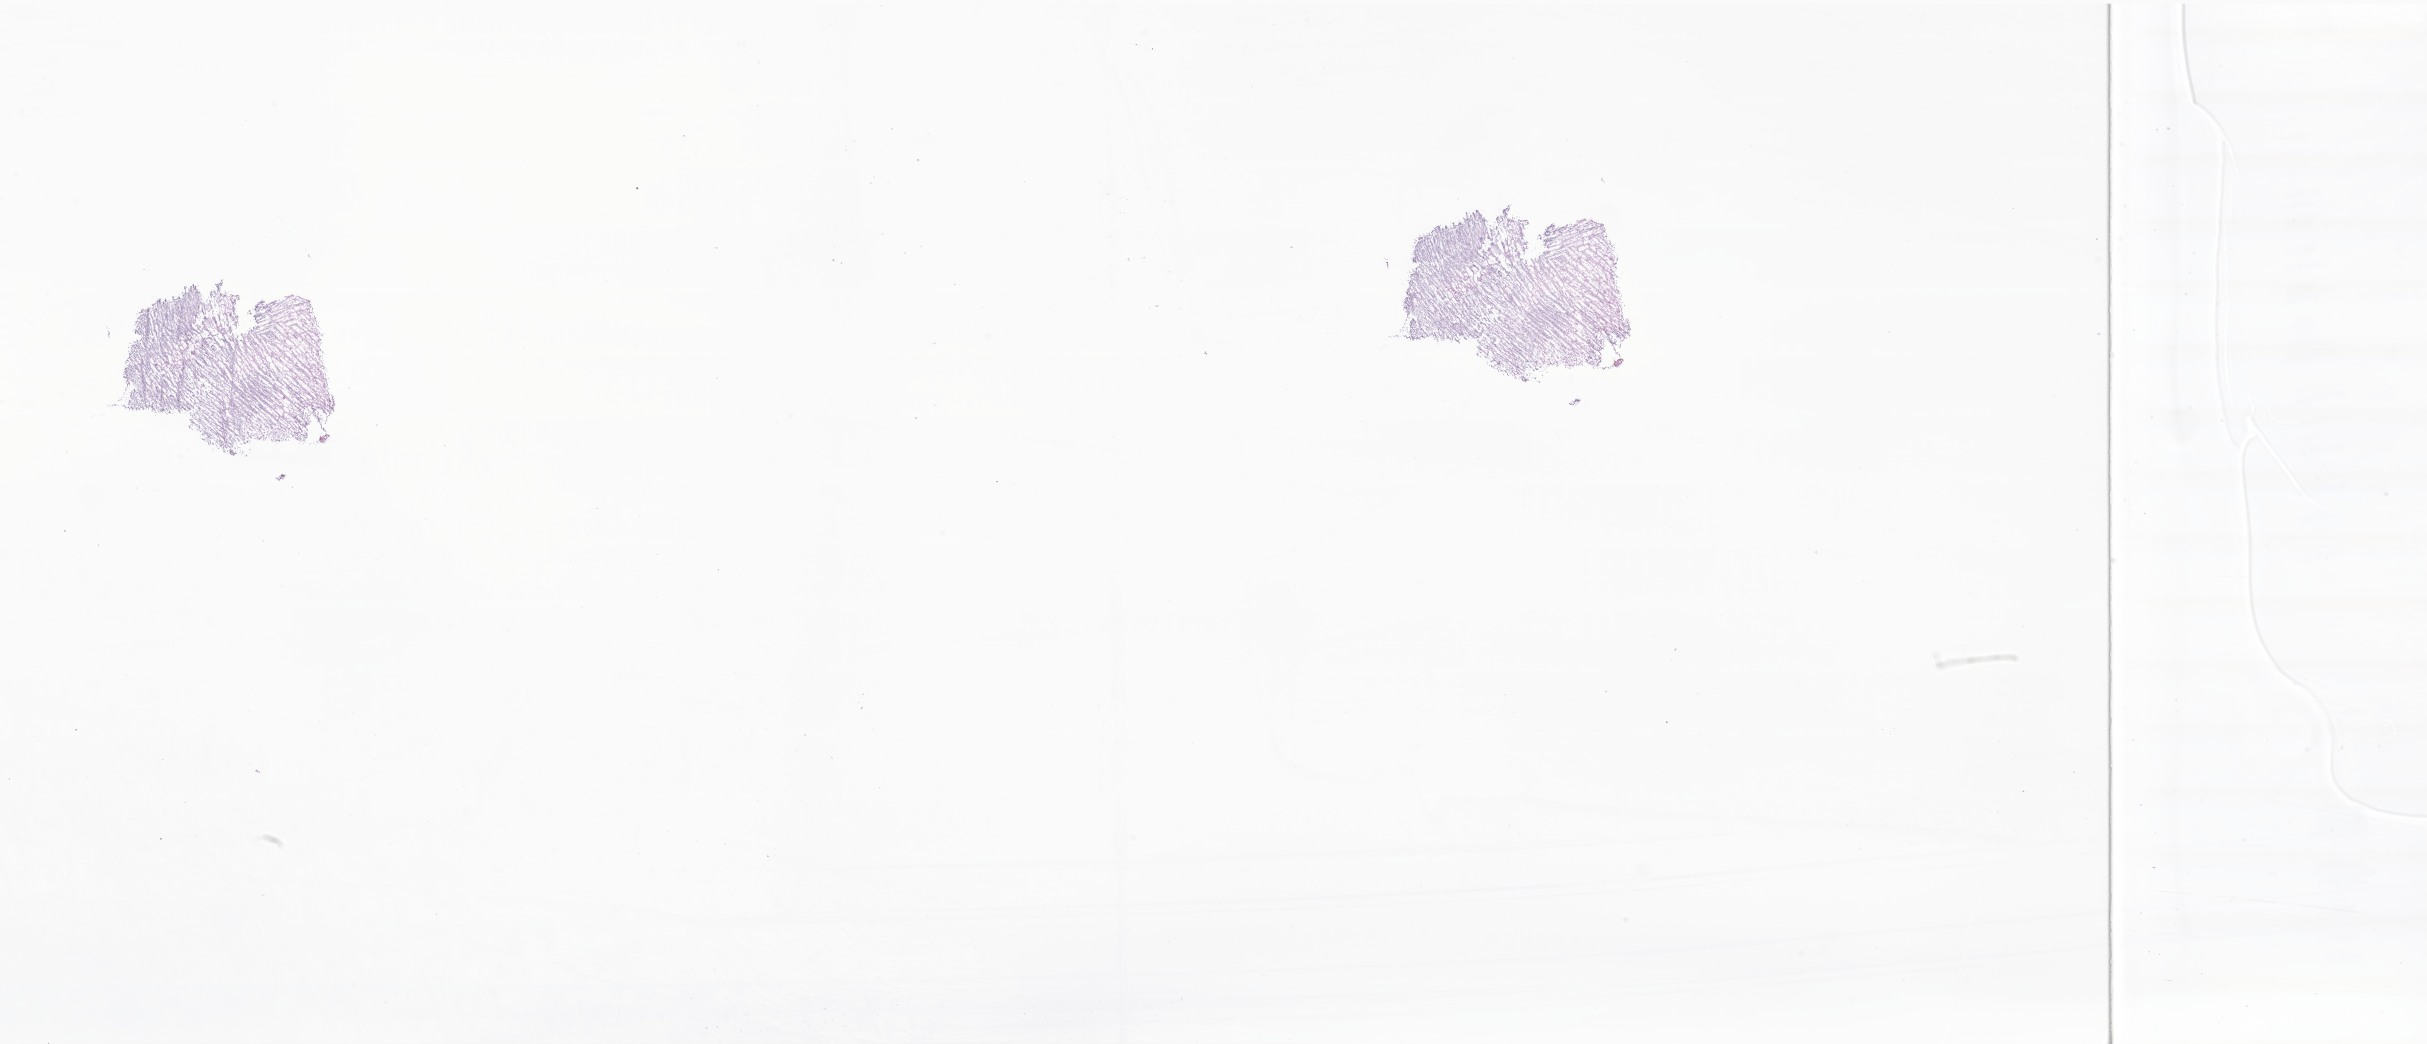
Digitized H&E-stained section of tumor tissue from the brain — shown as a low-resolution overview of the whole scanned area (about 40.9 x 17.6 mm); cryosection (OCT / tissue freezing medium). Patient male; age 102 months.
- diagnosis (ICD-O-3 morphology term): Medulloblastoma, NOS